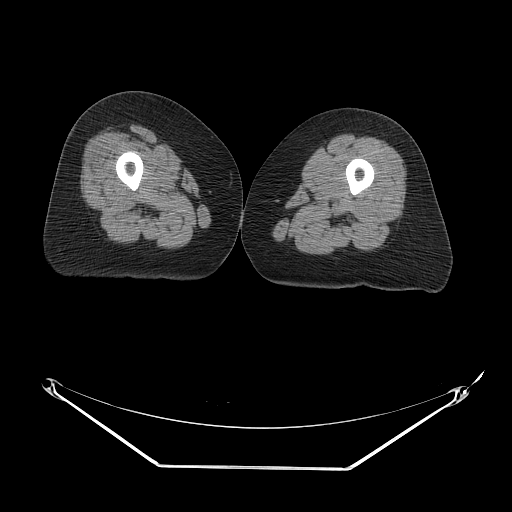
CT of an extremity soft-tissue mass (from a PET/CT study), one axial slice. Slice 11 of 267 in the series (ordered by position). Reconstruction kernel STANDARD. 140 kVp. Soft-tissue window (W 400 / L 40 HU). 3.75 mm slice thickness. 512 × 512 image matrix, field of view 500 × 500 mm. Female patient. Case-level facts recorded for this patient, not image findings: histological type: malignant solitary fibrous tumor; grade: intermediate; site of the primary tumour: right thigh.
Annotated regions visible in this slice (expert contour drawn on MRI and transferred to this co-registered scan by the dataset authors):
- gross tumour volume including surrounding oedema: bounding box (x1, y1, x2, y2) in pixels: (135, 132, 181, 161)